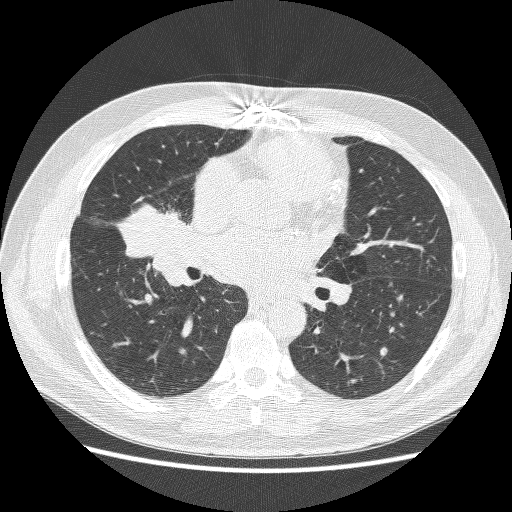
Low-dose screening chest CT, axial slice, baseline annual screen, lung window (W 1500 / L -600 HU), lung (sharp) reconstruction kernel (BONE). Male, age 59 years at enrolment.
Lesion marked by an expert reader, box from (x=122, y=190) to (x=197, y=263) px. No non-calcified nodule or mass ≥4 mm was recorded by the screening reader at this exam. Official screen result: positive, change unspecified: nodule(s) >= 4 mm or enlarging nodule(s), mass(es), or other non-specific abnormalities suspicious for lung cancer. Later outcome: lung cancer diagnosed 24 days after this screen — adenocarcinoma, NOS, right middle lobe, poorly differentiated (G3), stage IV (AJCC 6th edition), 54 mm at pathology.